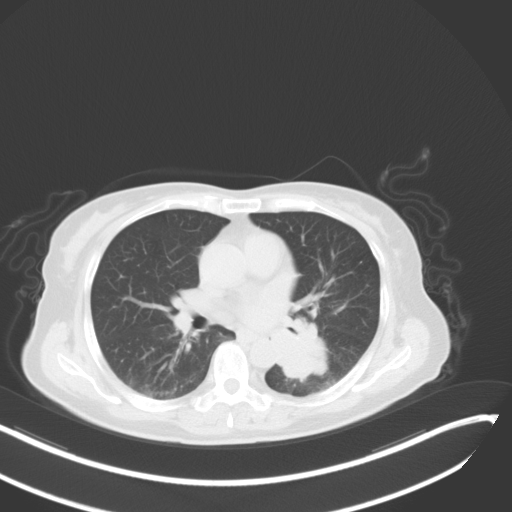
Chest CT, one axial slice; slice 20 of 48 in the series (ordered by position); reconstruction kernel B31f; lung window (W 1500 / L -600 HU); 512 × 512 image matrix, field of view 400 × 400 mm. Female patient, age 64 years. From the clinical record (not read from this slice): clinical TNM (as recorded): T3 N1 M1.
Structures marked on this image (rectangle marked by the reading radiologist):
- lung tumour (recorded histology: small cell carcinoma): box from (x=269, y=313) to (x=335, y=384) px